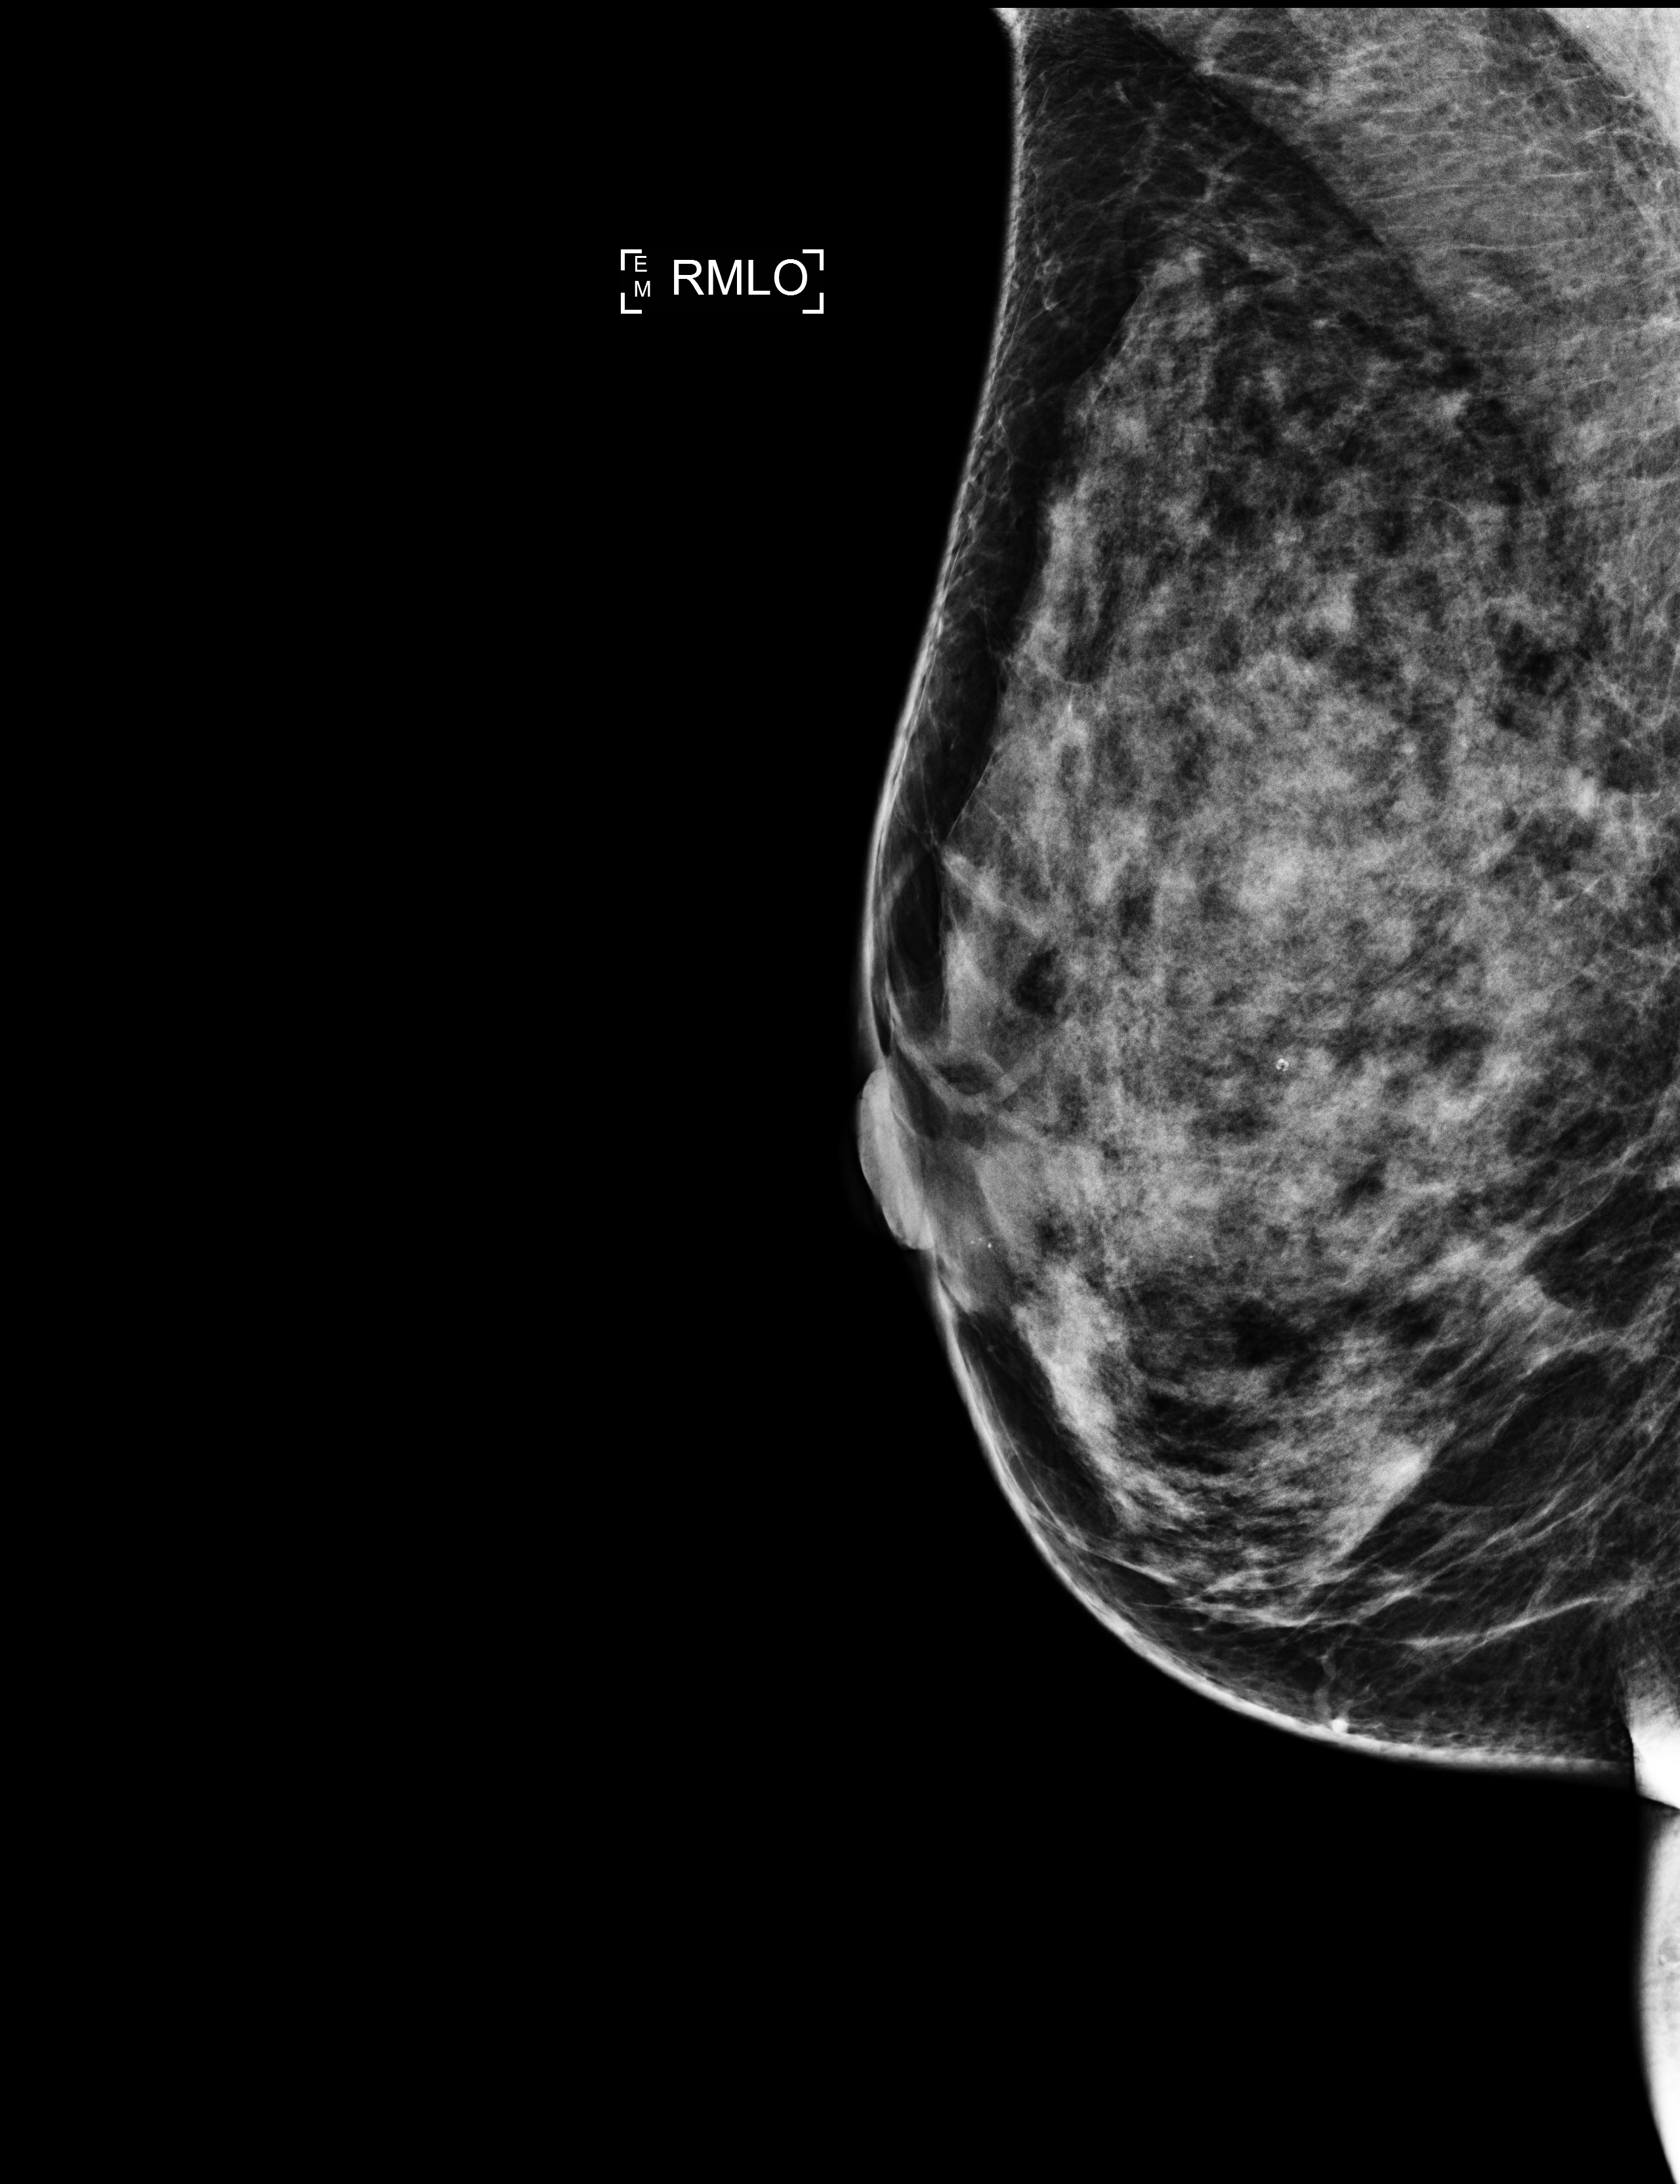
Annual screening mammography examination. Patient aged 44 years (female).
Image type: full-field digital mammogram. Breast: right. Projection: MLO view.